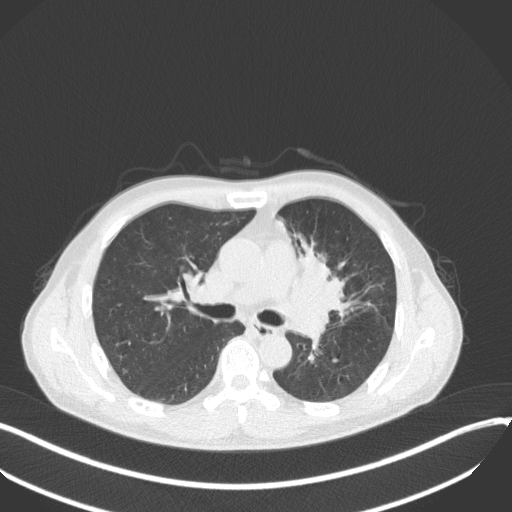
Chest CT, one axial slice. Slice 204 of 411 in the series (ordered by position). 120 kVp. Lung window (W 1500 / L -600 HU). 512 × 512 image matrix, field of view 400 × 400 mm. Male patient, age 56 years. Case-level facts recorded for this patient, not image findings: clinical TNM (as recorded): T2a N0 M0.
Annotated regions visible in this slice (rectangle marked by the reading radiologist):
- lung tumour (recorded histology: squamous cell carcinoma): bounding box [x1, y1, x2, y2] px = [288, 232, 358, 328]